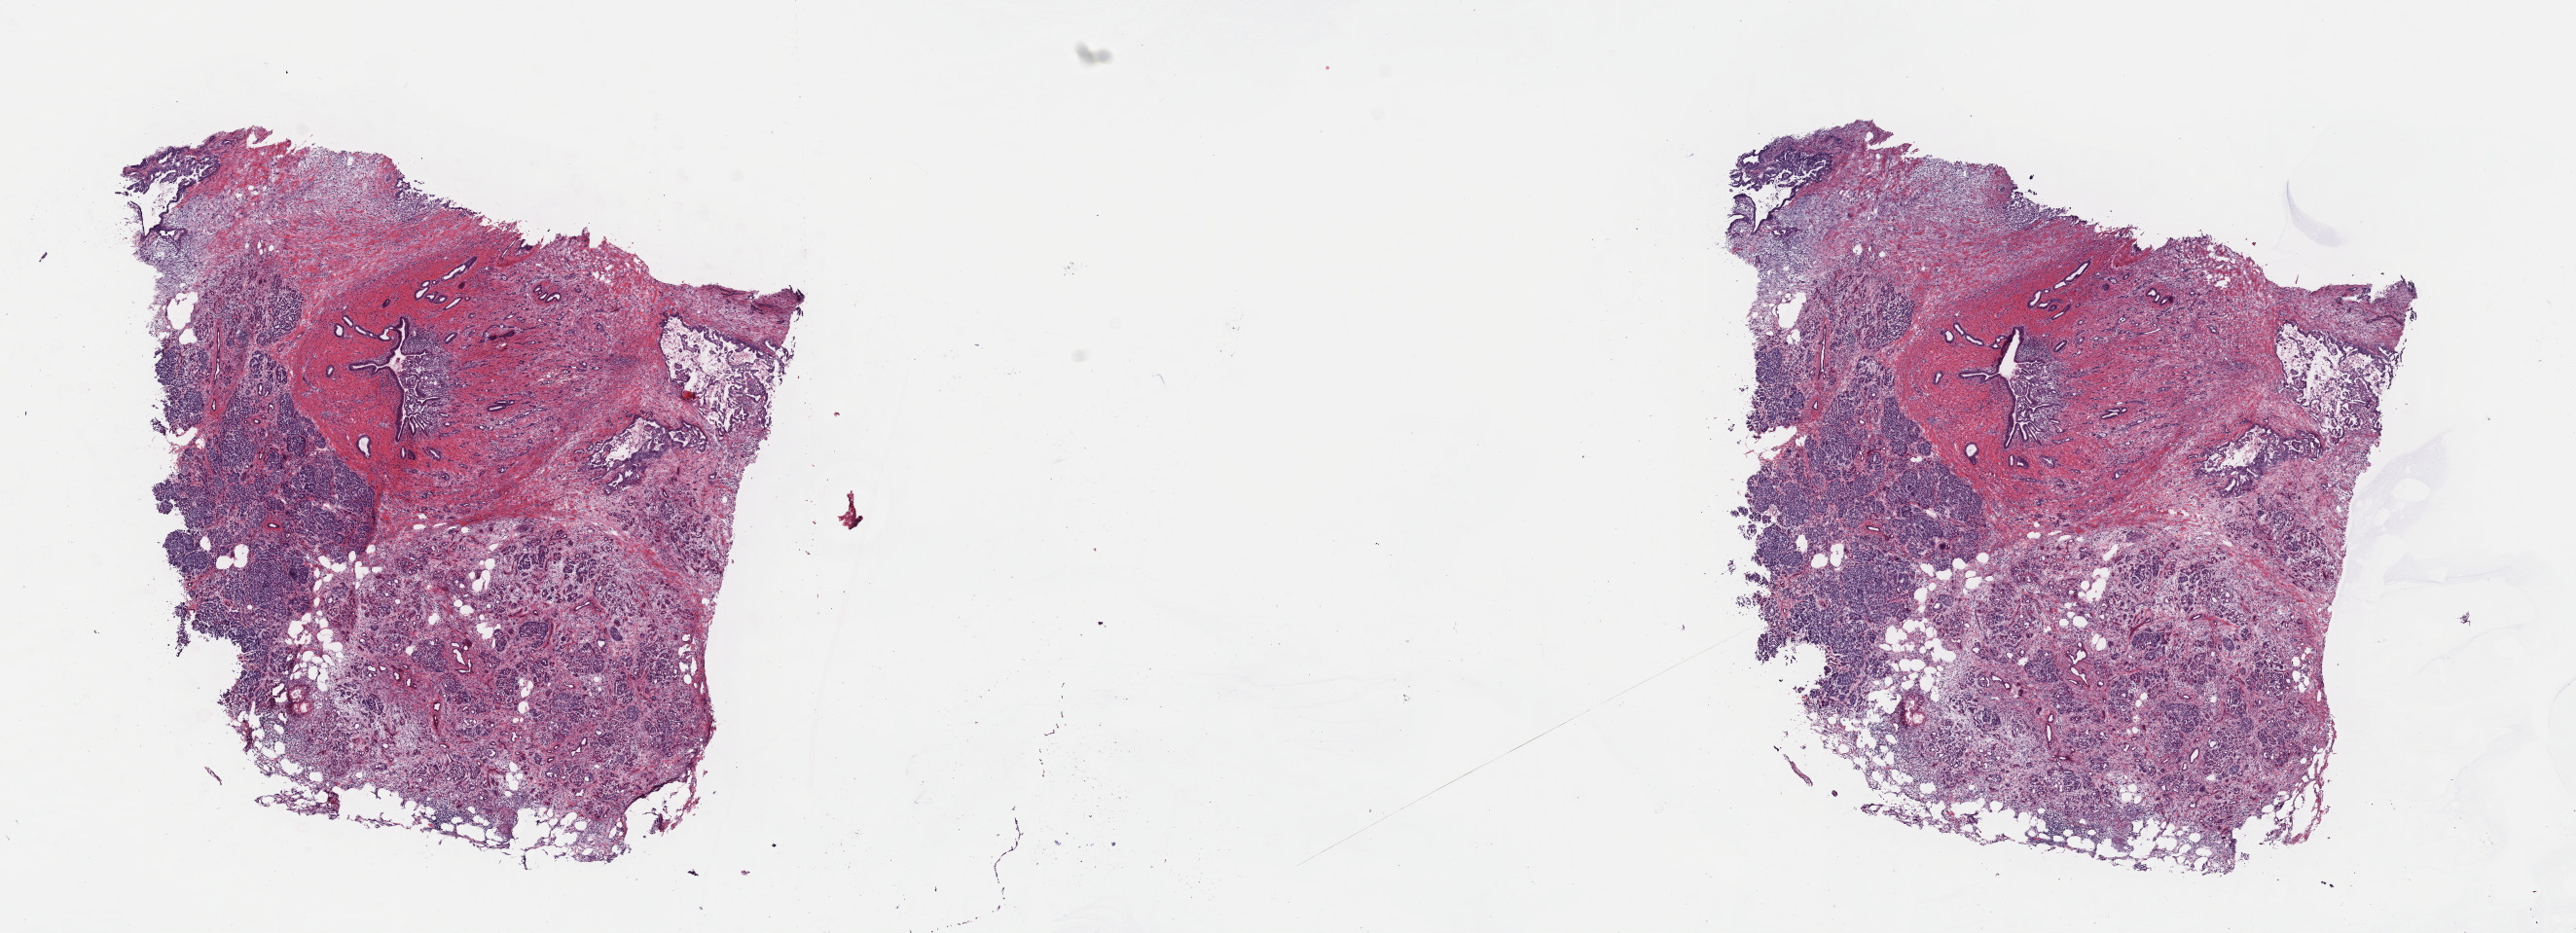
Digitized H&E tissue section (whole slide), low-resolution overview of the scanned area, about 20.9 x 7.6 mm. Frozen section from the top of the tissue portion. Primary tumour sample from the pancreas. Patient: male, age at initial diagnosis 54 years. Pathologist review of this section (percent, as recorded): tumour cells 30%, tumour nuclei 40%.
Pathologic diagnosis: Infiltrating duct carcinoma, NOS (head of pancreas).